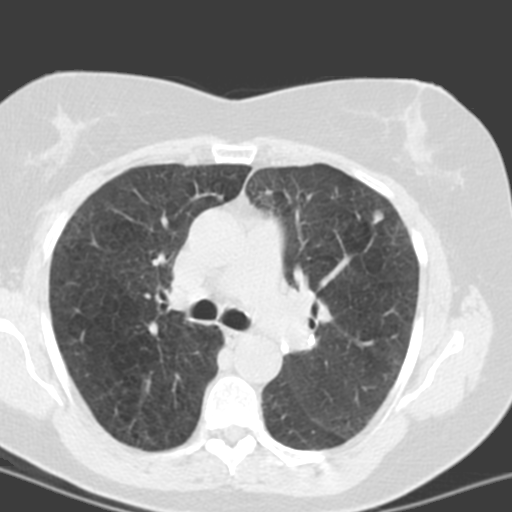
Low-dose screening chest CT, one axial slice; slice 102 of 150 in the series (ordered by position); lung window (W 1500 / L -600 HU); 3.2 mm slice thickness; 512 × 512 image matrix, field of view 290 × 290 mm.
Structures marked on this image (outlined manually by an expert reader):
- lesion 1 (tumor, lower lobe of left lung): box from (x=374, y=209) to (x=386, y=223) px